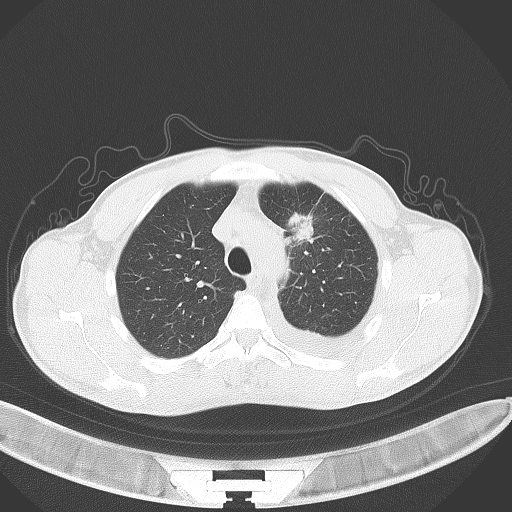
Chest CT, one axial slice; position 102 of 130 along the scan axis; reconstruction kernel B70f; 120 kVp; lung window (W 1500 / L -600 HU); 3 mm slice thickness; 512 × 512 image matrix. Patient: male, 49 years. Case-level facts recorded for this patient, not image findings: clinical TNM (as recorded): T1c N1 M1.
Outlined on this slice (rectangle marked by the reading radiologist):
- lung tumour (recorded histology: adenocarcinoma): box from (x=285, y=212) to (x=318, y=246) px